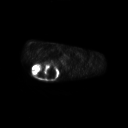
FDG PET of an extremity soft-tissue mass (from a PET/CT study), one axial slice; slice 199 of 267 in the series (ordered by position); 3.27 mm slice thickness; 128 × 128 image matrix. Patient: male, 61 years. From the clinical record (not read from this slice): histological type: pleiomorphic spindle cell undifferentiated; grade: high; site of the primary tumour: right parascapusular.
Structures marked on this image (expert contour drawn on MRI and transferred to this co-registered scan by the dataset authors):
- gross tumour volume including surrounding oedema: bounding box <31,63,61,78> (left, top, right, bottom; pixels)
- gross tumour volume (mass): <31,63,58,78>